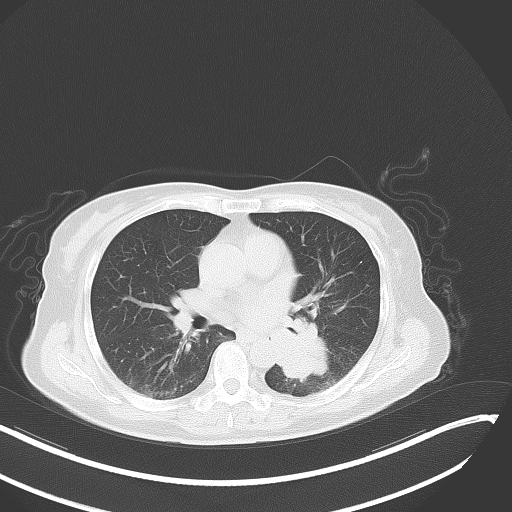
Chest CT, one axial slice. Slice 20 of 48 in the series (ordered by position). 120 kVp. Lung window (W 1500 / L -600 HU). 5 mm slice thickness. 512 × 512 image matrix, field of view 400 × 400 mm. Patient: female, 64 years. From the clinical record (not read from this slice): clinical TNM (as recorded): T3 N1 M1; histopathological grade: G3.
Structures marked on this image (bounding box drawn by a radiologist):
- lung tumour (recorded histology: small cell carcinoma): bounding box [x1, y1, x2, y2] px = [261, 309, 326, 378]